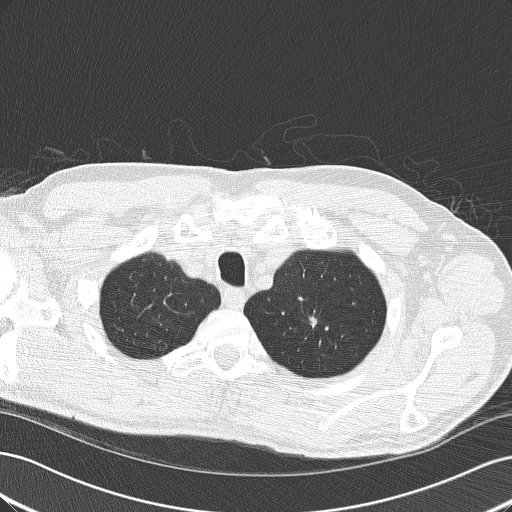
Low-dose screening chest CT, one axial slice; position 159 of 189 along the scan axis; lung window (W 1500 / L -600 HU); 2 mm slice thickness; 512 × 512 image matrix, field of view 360 × 360 mm.
Outlined on this slice (expert manual segmentation):
- lesion 1 (tumor, upper lobe of left lung): bounding box [x1, y1, x2, y2] px = [312, 314, 316, 329]